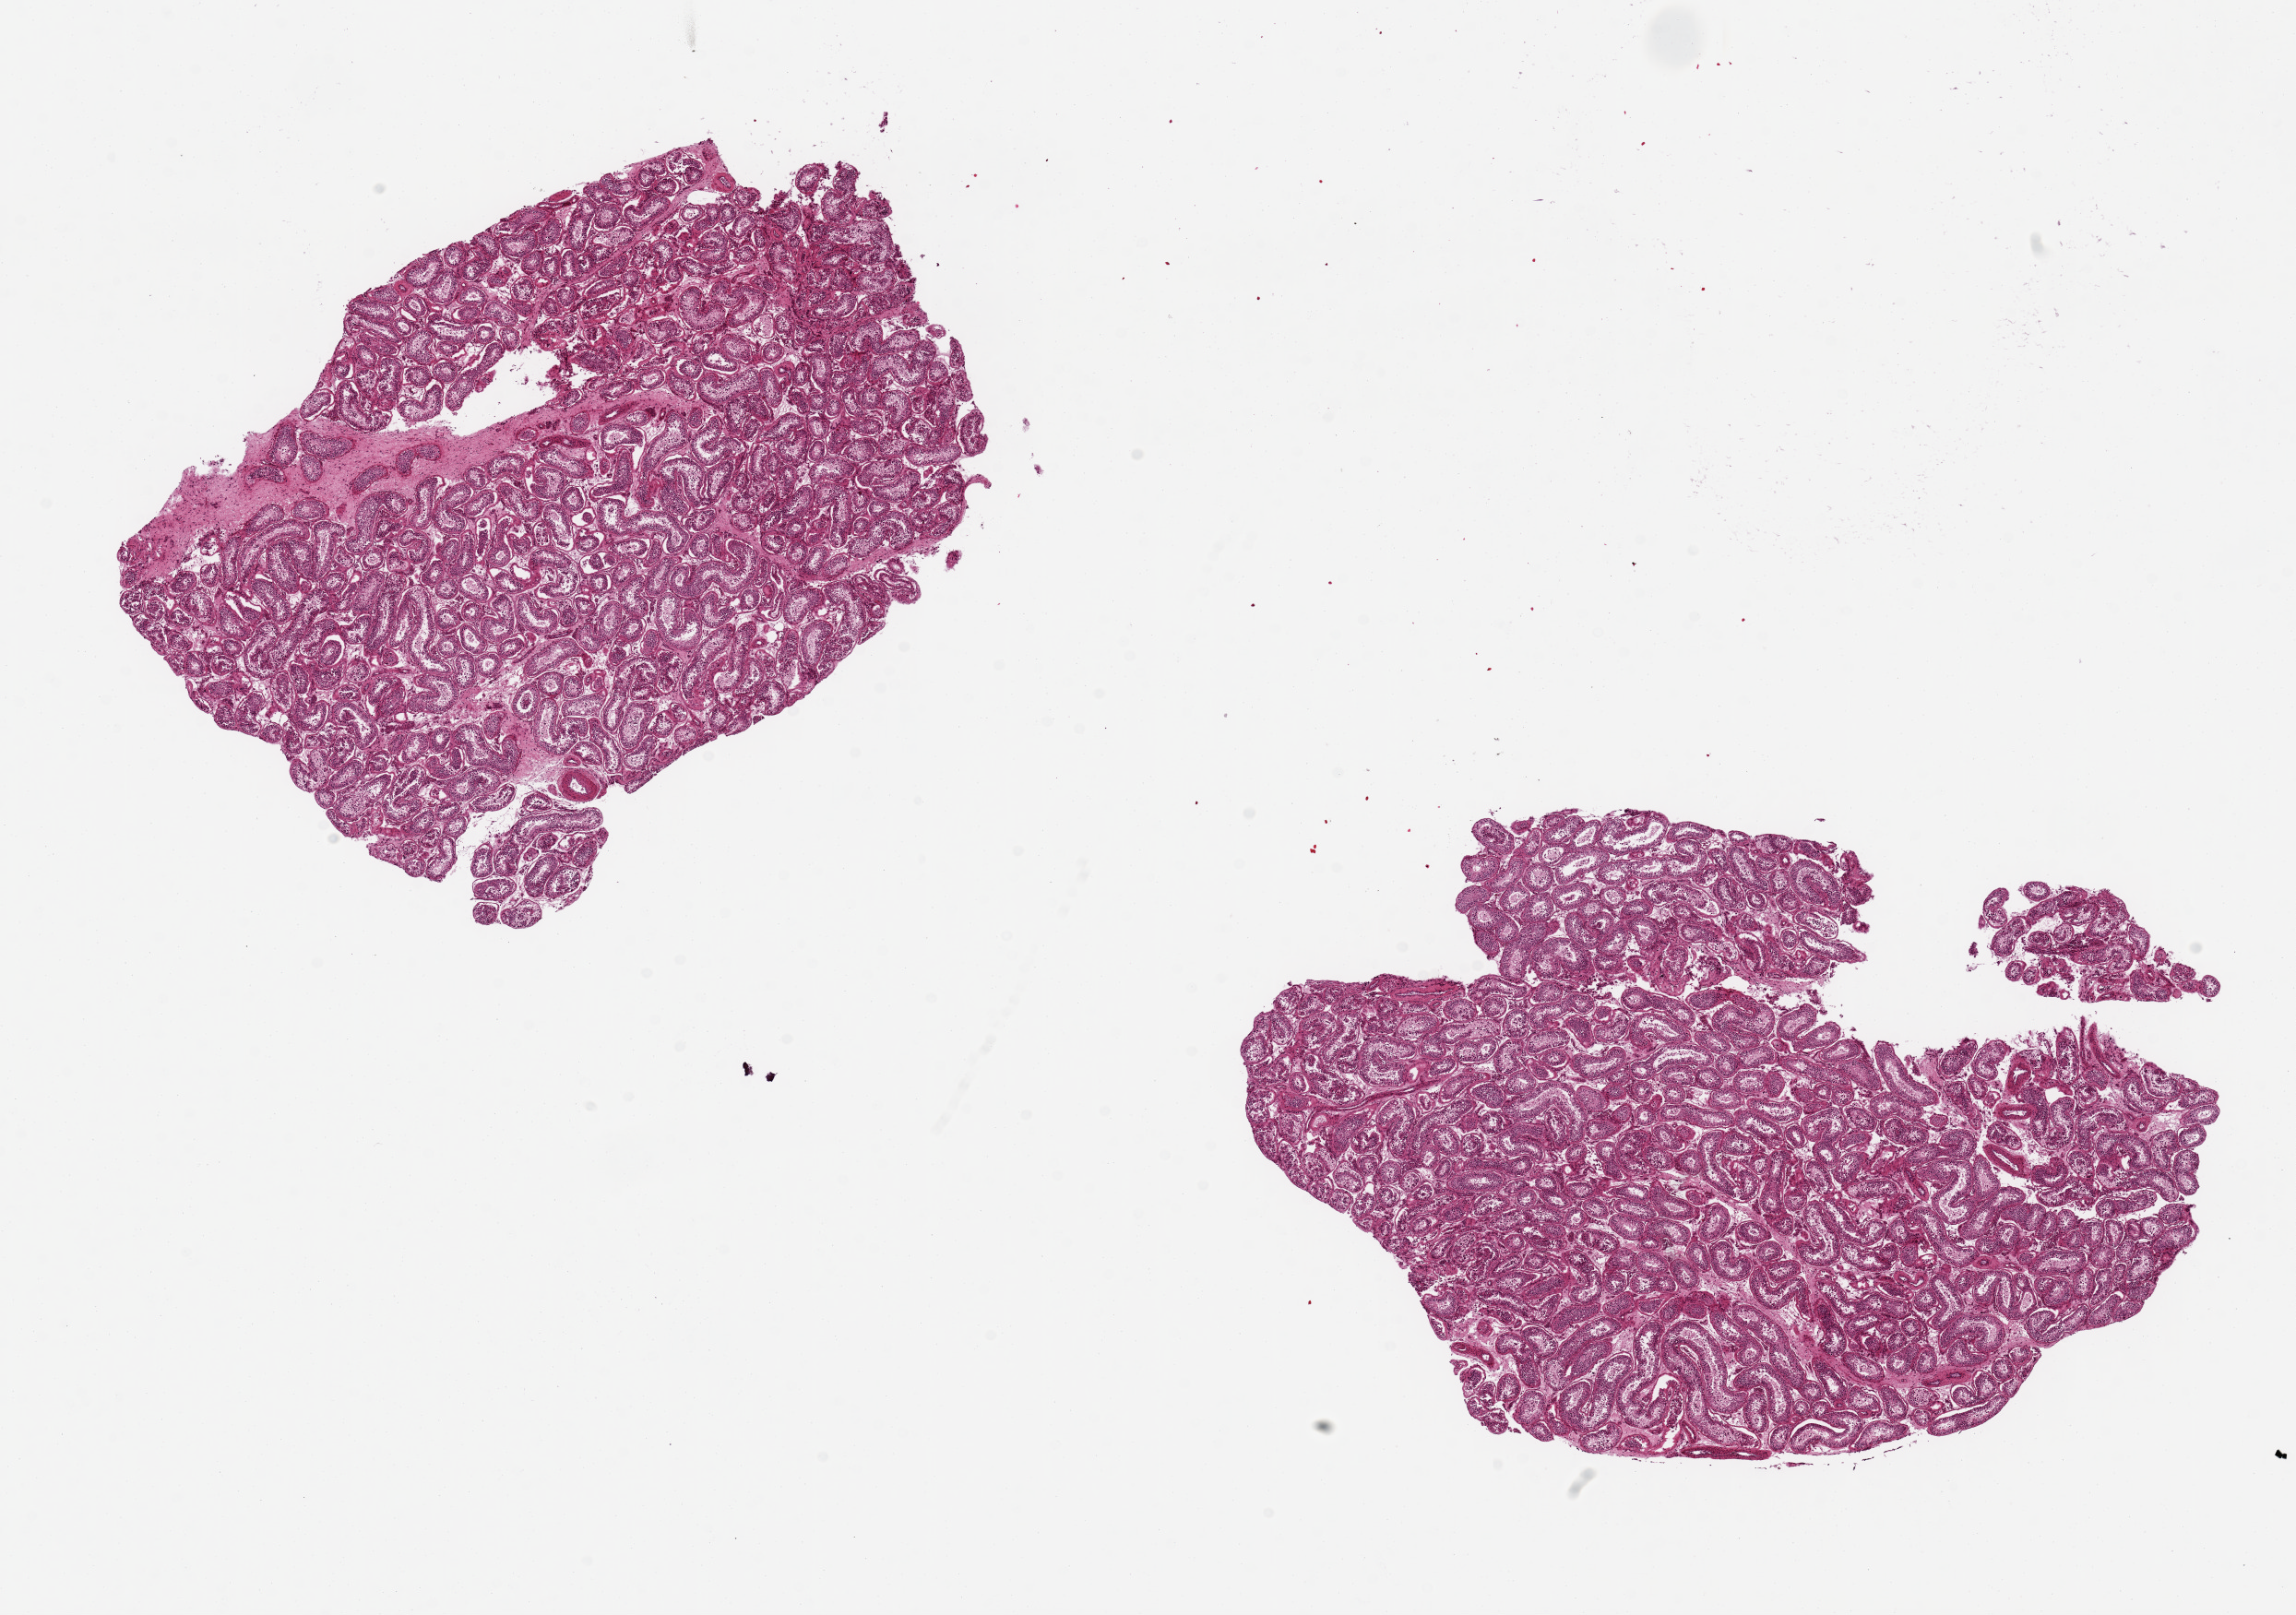
Whole-slide image, hematoxylin and eosin (H&E) stain, brightfield — a low-resolution overview of the entire scanned area, about 19.7 x 13.9 mm (from a 20x scan). PAXgene-fixed paraffin-embedded (PFPE) section. Target tissue: testis. Tissue donor sample. Male donor.
Pathologist's review note for this sample: 2 pieces 7x5mm. Spermatogenesis present.